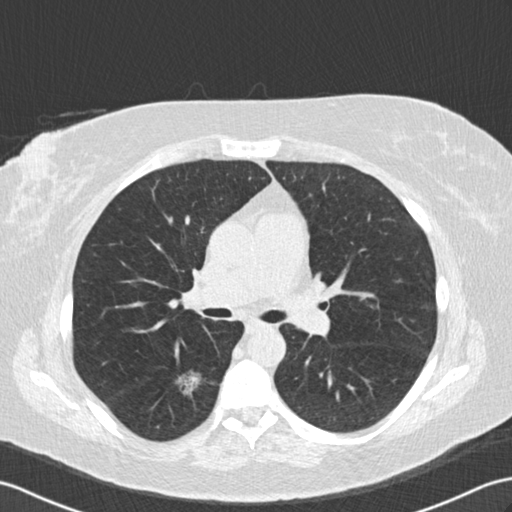
Axial slice from a low-dose chest CT screening exam; second annual screen; lung window (W 1500 / L -600 HU); 2 mm slice thickness. Female participant, aged 65 years at enrolment. Former smoker at enrolment.
Lesion marked by an expert reader, box from (x=157, y=356) to (x=214, y=412) px. Reader record for this screening exam (exam-level; its link to the box is not recorded): non-calcified nodule or mass ≥4 mm, right lower lobe, 18 × 16 mm, spiculated (stellate) margins, soft tissue attenuation, pre-existing on the prior screen: yes; interval growth: yes. Official screen result: positive, other. Participant outcome: lung cancer diagnosed 239 days after this screen — adenocarcinoma, NOS, right lower lobe, moderately differentiated (G2), stage IA (AJCC 6th edition), 25 mm at pathology.